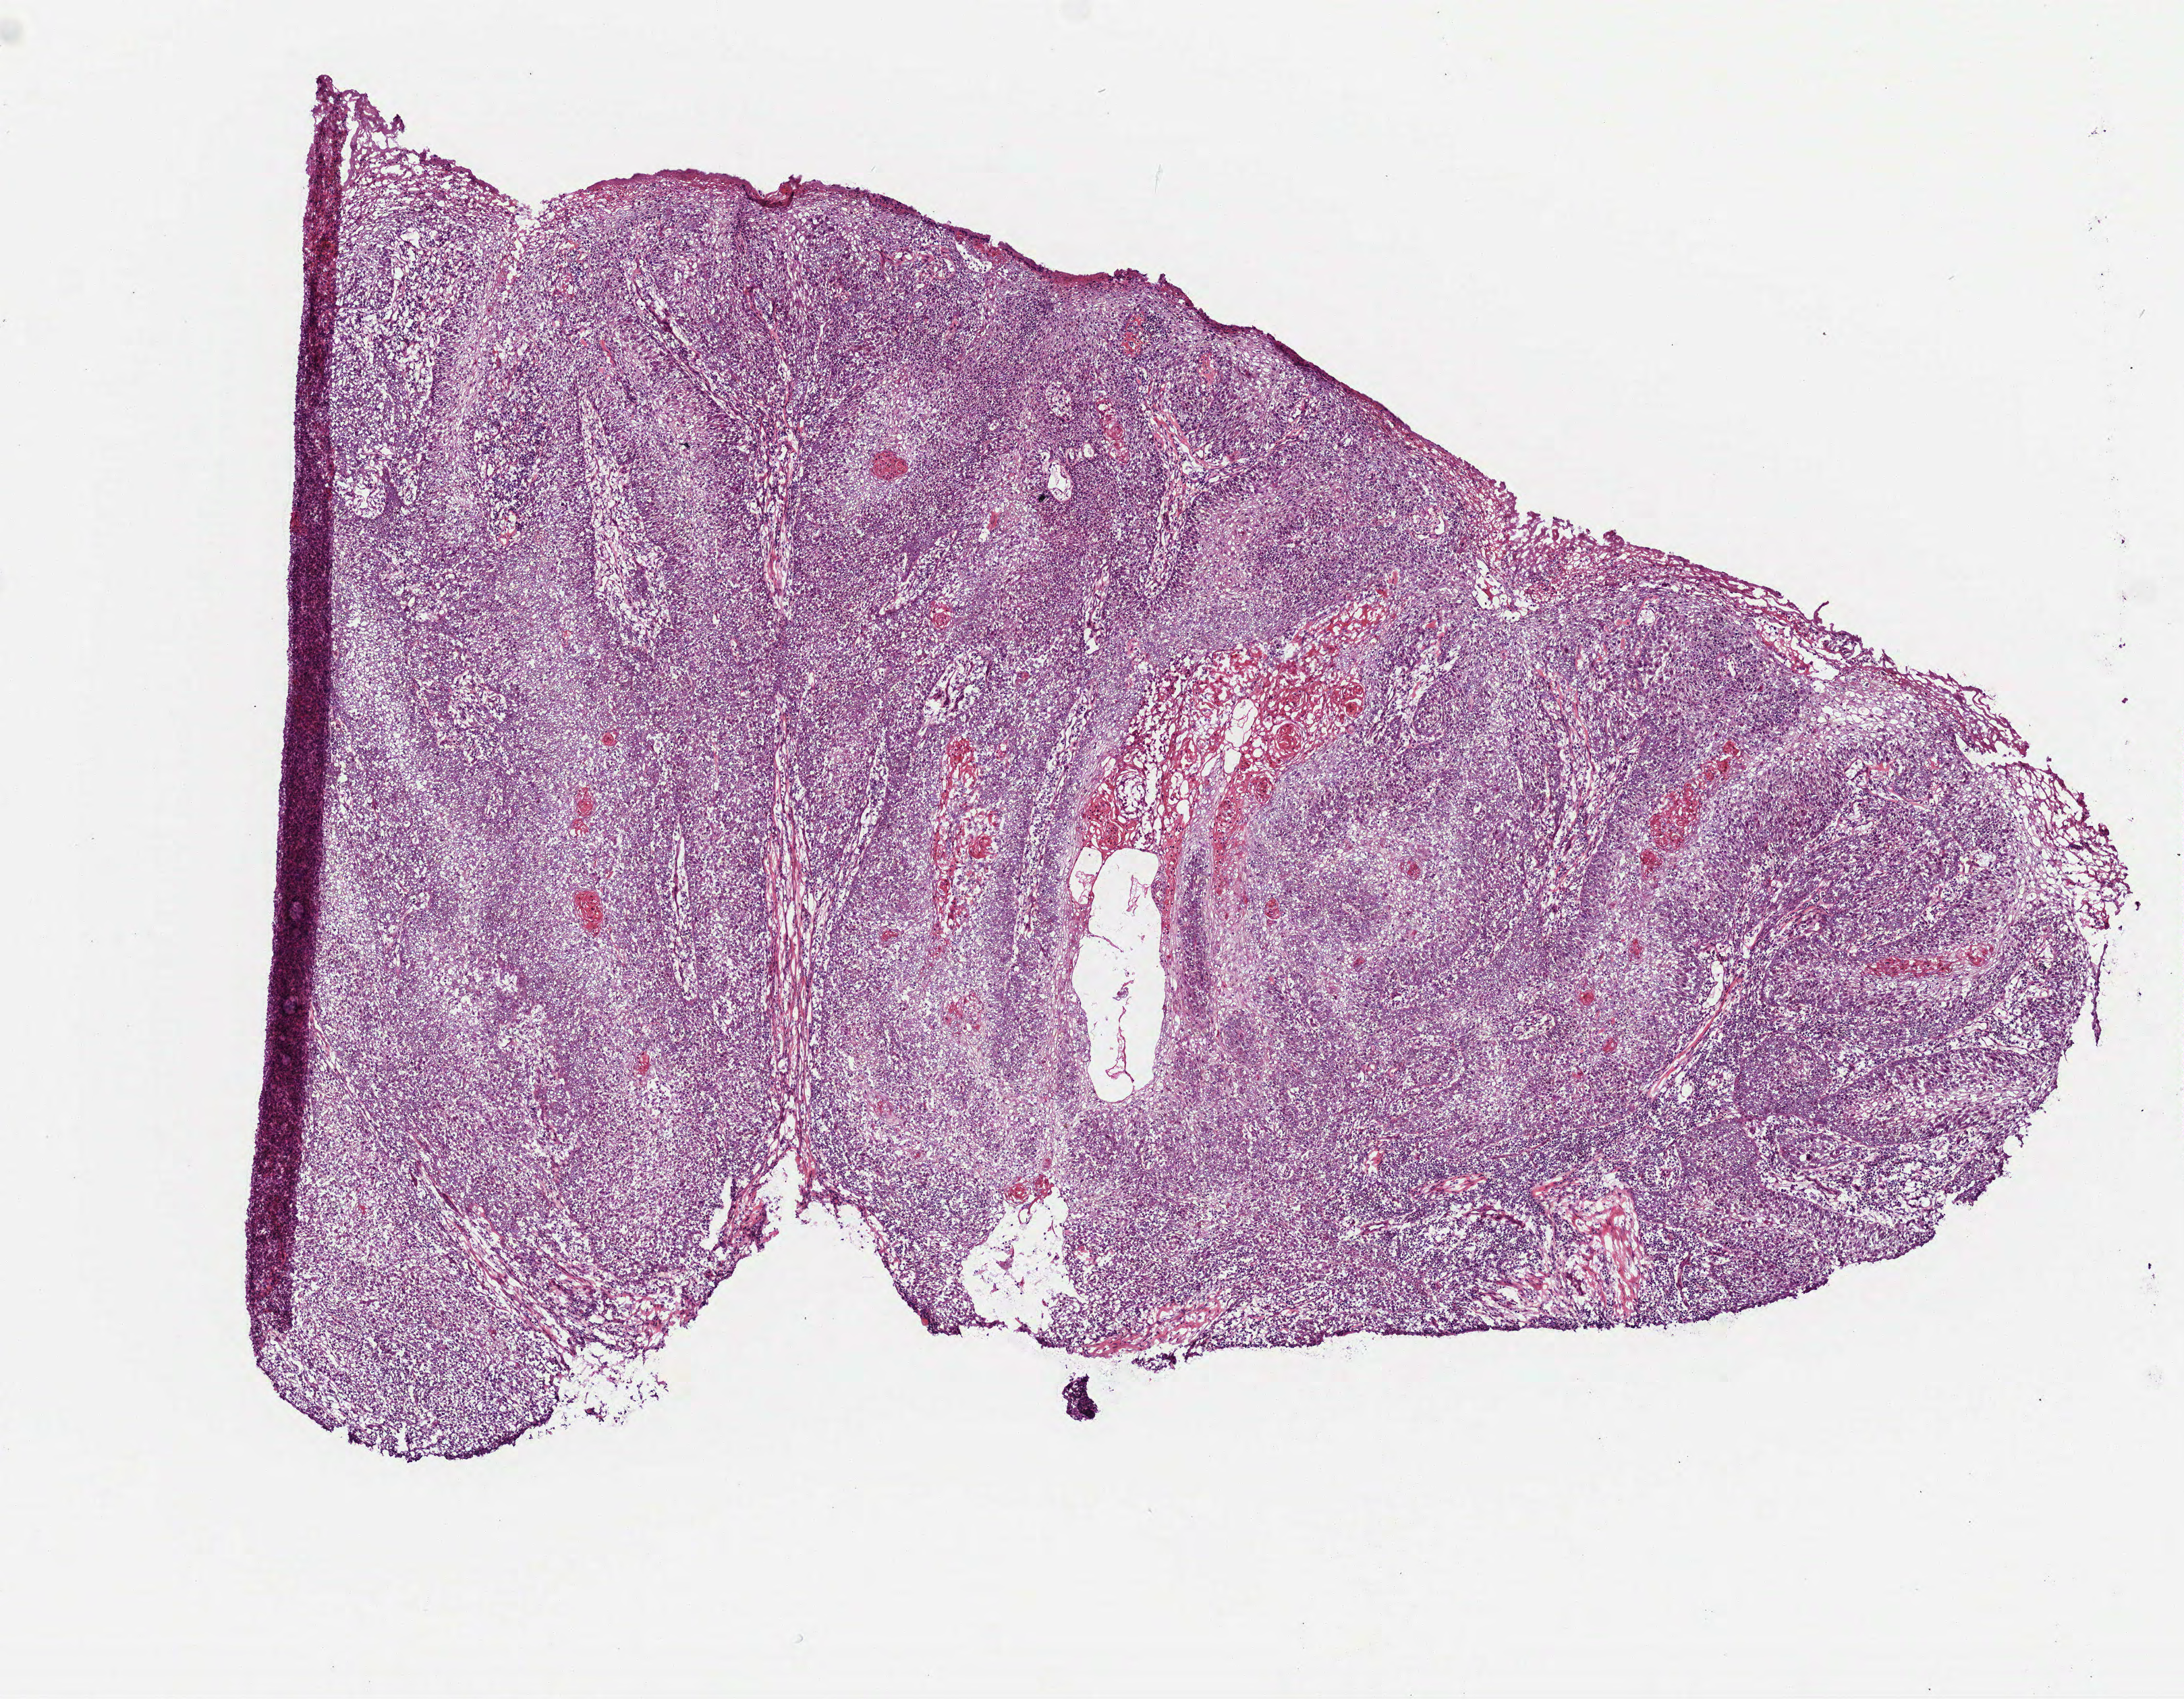
Digitized Hematoxylin and eosin (H&E) stained tissue section (whole slide), a low-resolution overview of the entire scanned area, about 6.5 x 5.1 mm (slide scanned at 40x), frozen section from the top of the tissue portion, sample: primary tumour, head and neck. Female, age 80 years at initial diagnosis. Histologic grade: G2 (moderately differentiated). Composition of this section per pathologist review: tumour cells 100%, tumour nuclei 75%, normal cells 0%, stromal cells 0%, necrosis 0%. Inflammatory infiltration, as recorded: lymphocyte infiltration 15%, monocyte infiltration 0%, neutrophil infiltration 2%.
- AJCC pathologic stage: II
- laterality: right
- pathologic diagnosis: Squamous cell carcinoma, NOS (overlapping lesion of lip, oral cavity and pharynx)